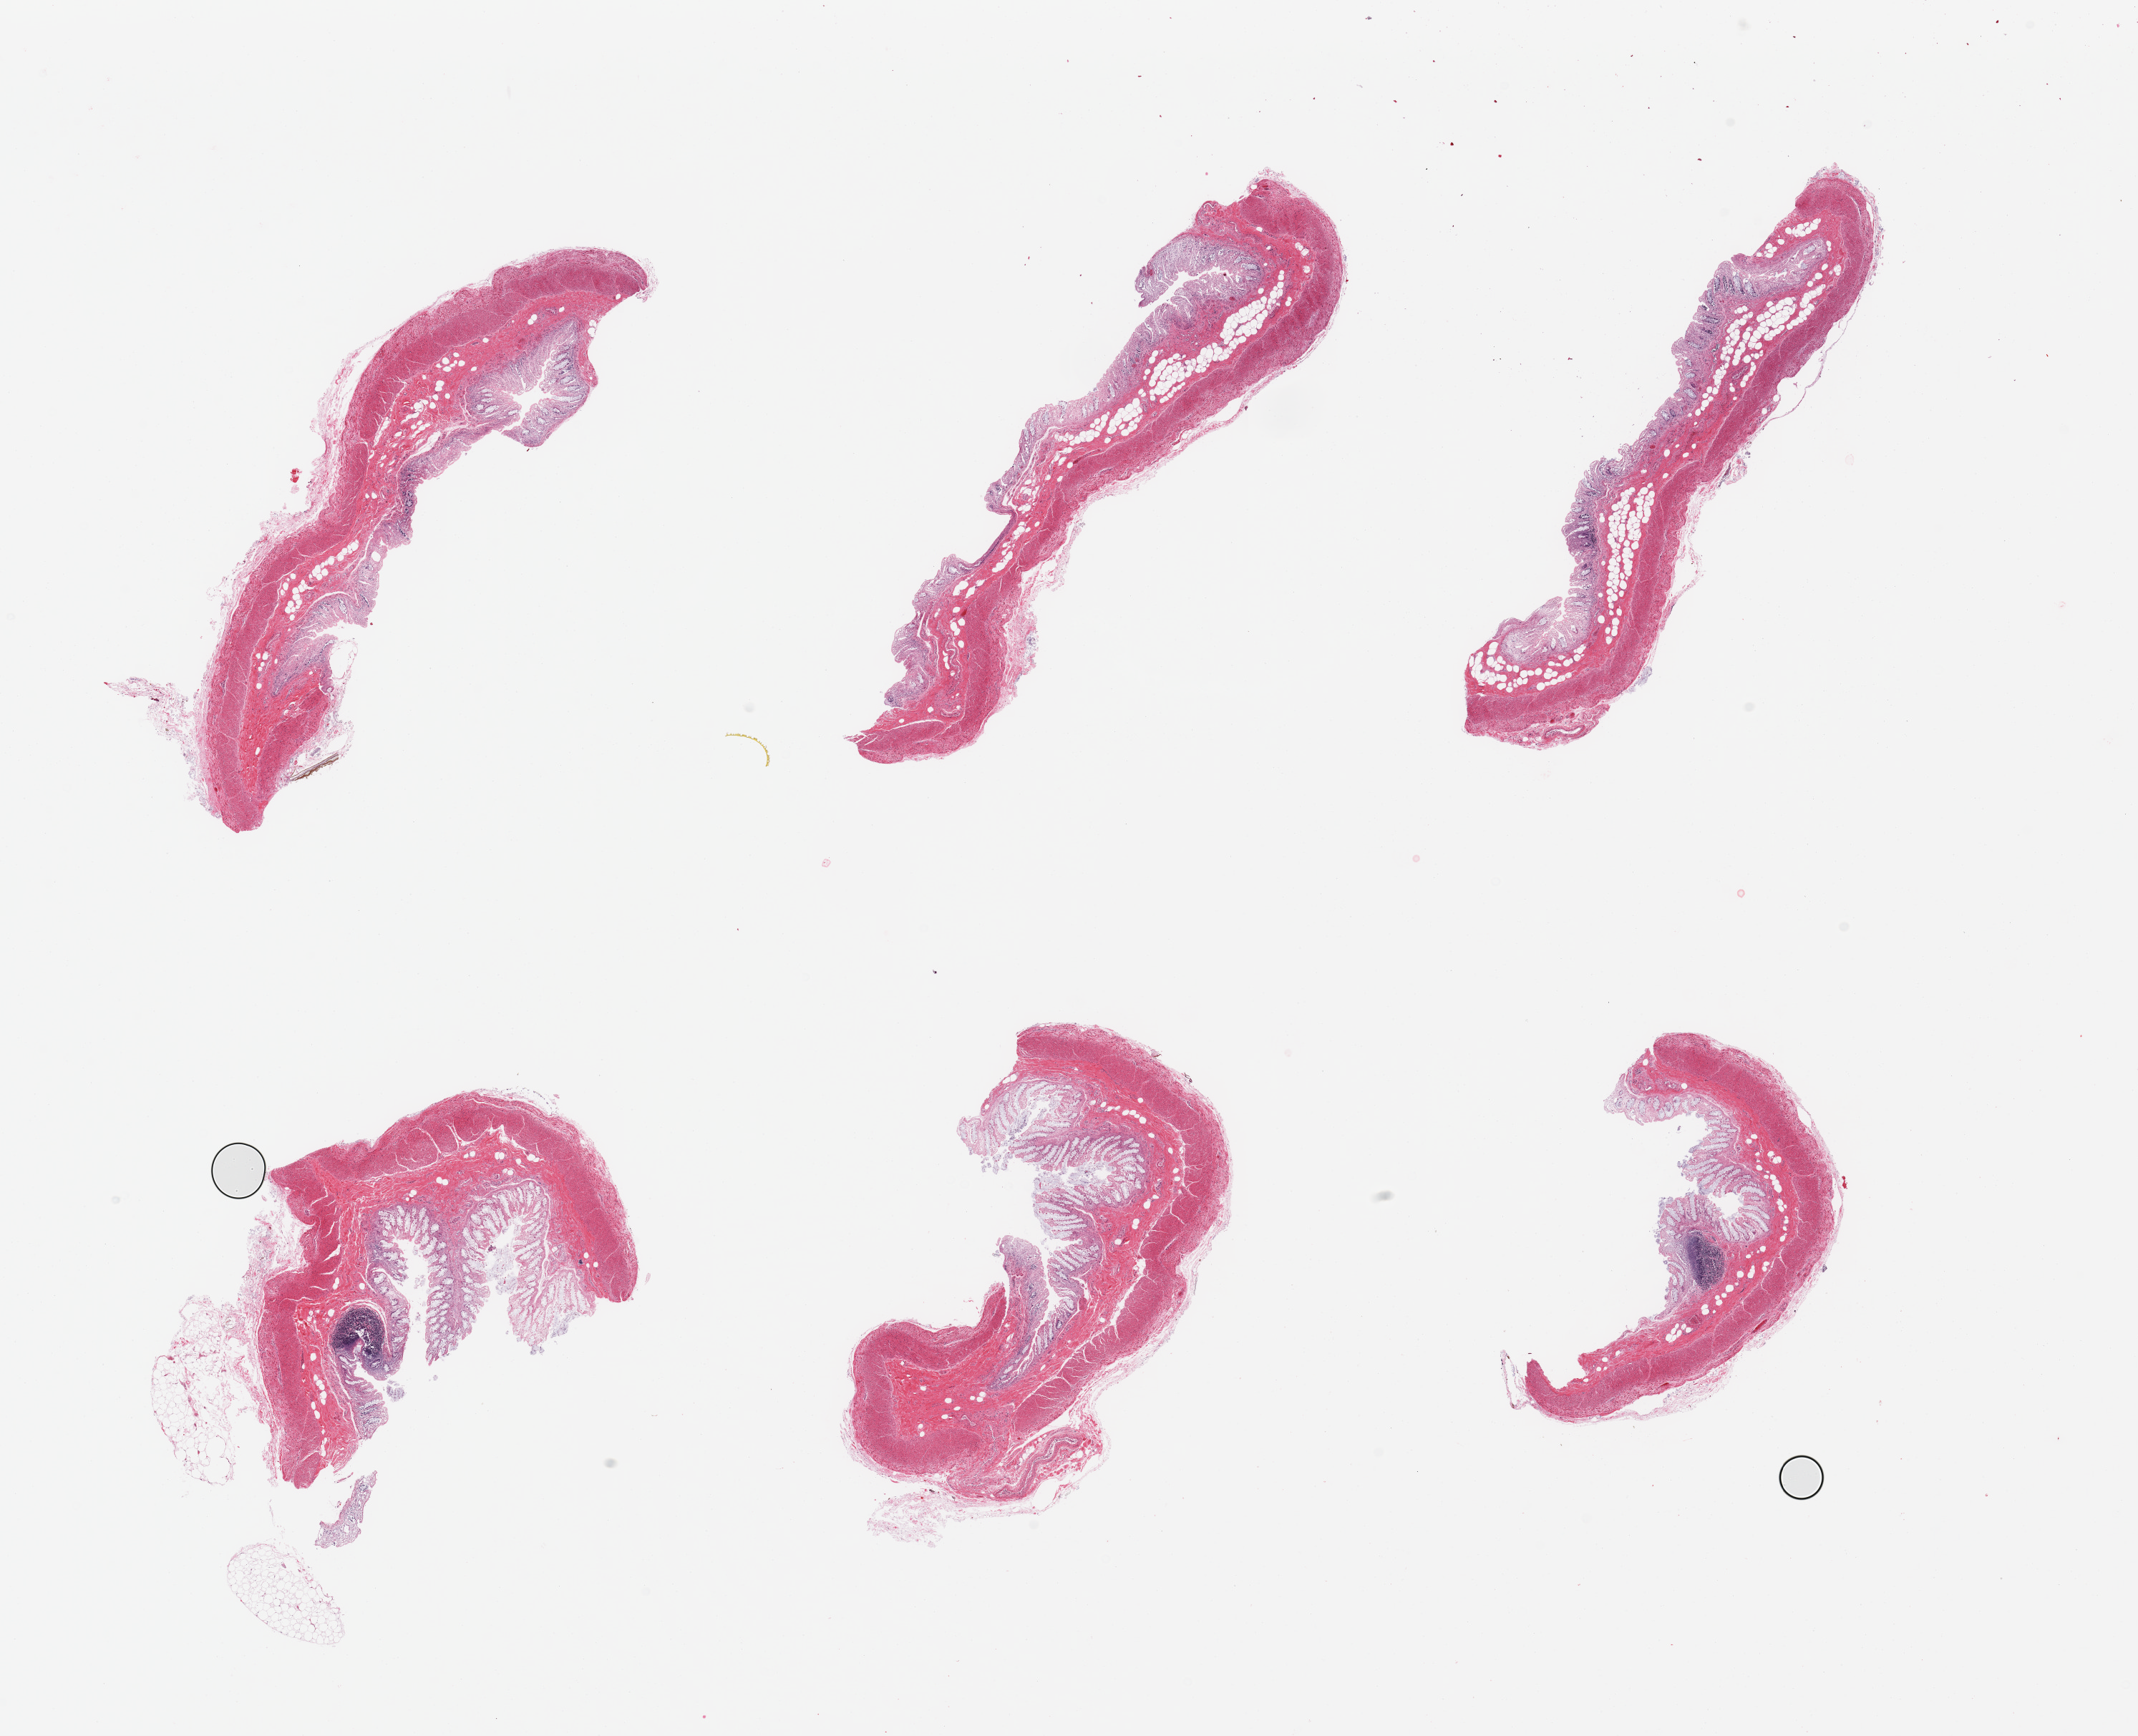
Whole-slide image, H&E stain — whole scanned area (about 23.6 x 19.2 mm, acquisition: 20x scan) shown as a low-resolution overview. PAXgene-fixed, paraffin-embedded tissue. Target tissue: transverse colon. Donor tissue sample. Donor: male.
• pathologist's review note for this sample: 6 pieces; full thickness sections, mucosa is severely autolyzed, but muscularis is better preserved